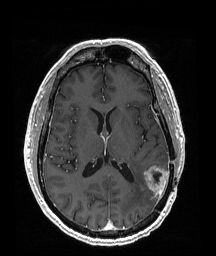
Brain MRI from a brain-tumour surgery series, one axial slice; position 86 of 192 along the scan axis; T1-weighted post-contrast; 1 mm slice thickness; 216 × 256 image matrix, field of view 211 × 250 mm. Case-level facts recorded for this patient, not image findings: histopathology: Glioblastoma; WHO grade: 4; IDH mutation: no; tumour location: Left Temporoparietal.
Annotated regions visible in this slice (manually delineated by an expert):
- tumour: bounding box <144,166,170,197> (left, top, right, bottom; pixels)